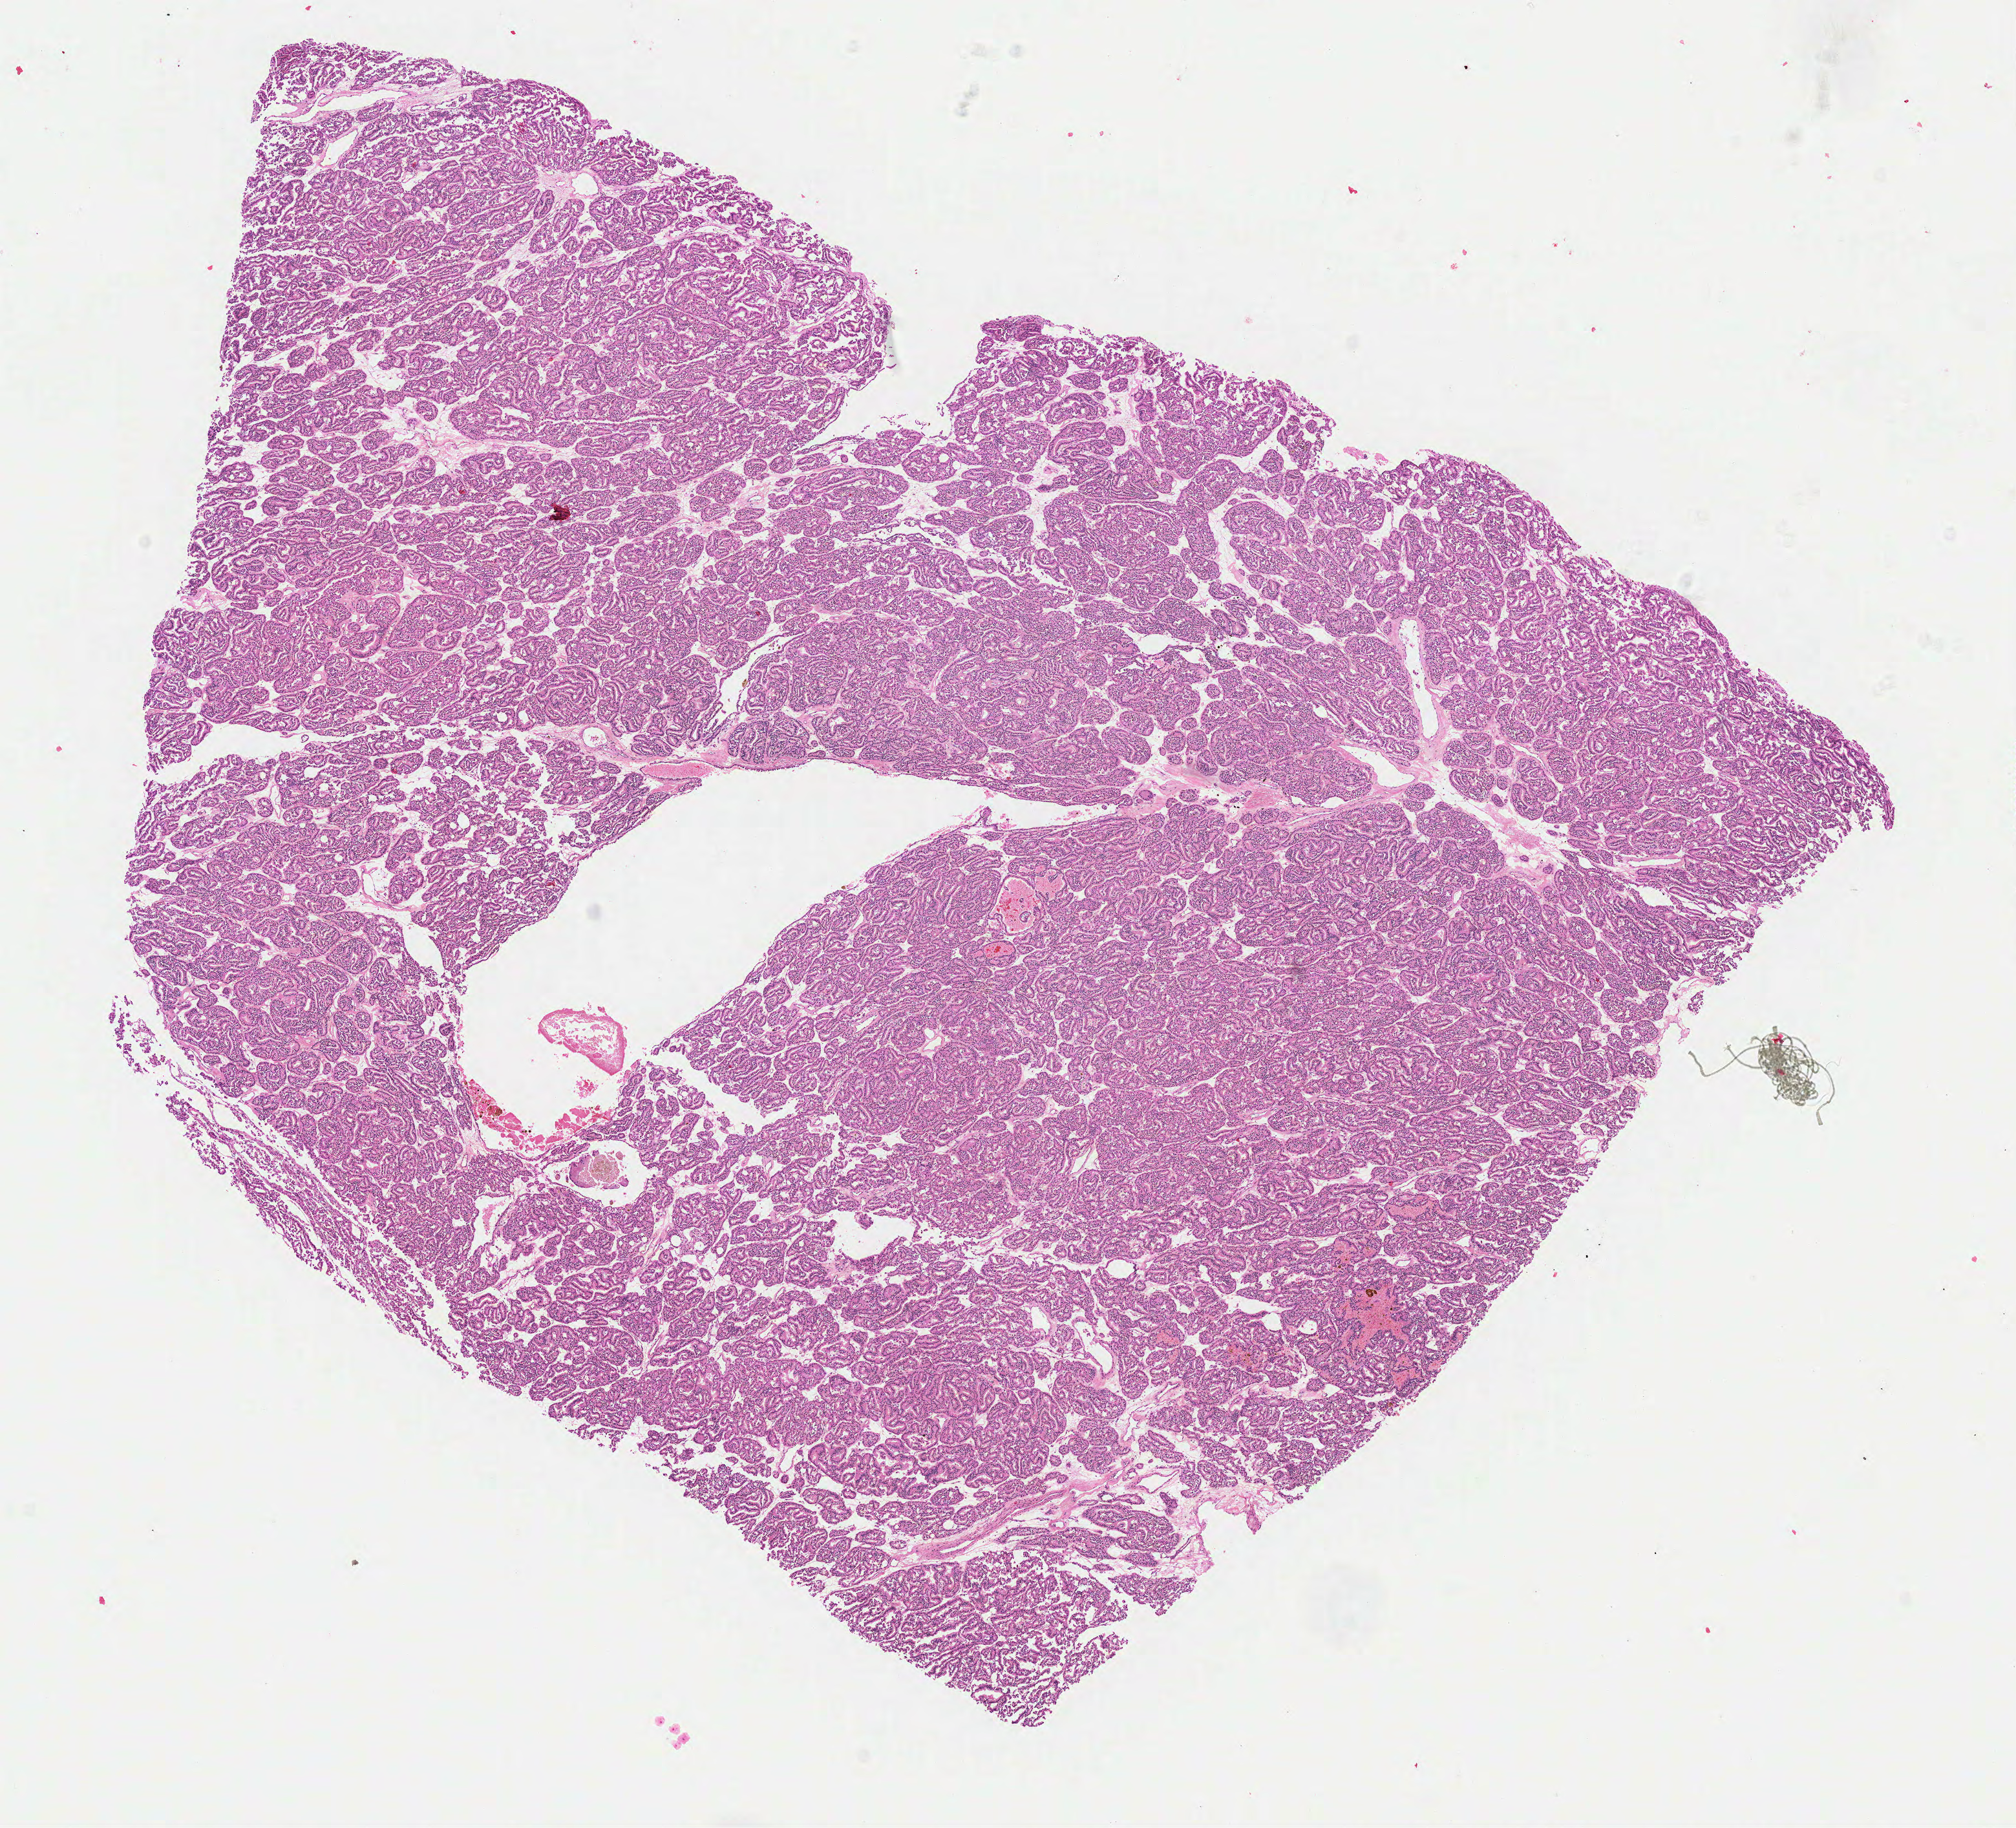
Whole-slide histology image, Hematoxylin and eosin (H&E) stained — a low-resolution overview of the entire scanned area, about 12.3 x 11.2 mm (from a 40x scan); formalin-fixed paraffin-embedded (FFPE) diagnostic section; primary tumour sample from the kidney. Male, age 45 years at initial diagnosis. Histologic grade: GX (grade cannot be assessed).
AJCC pathologic stage: II. Pathologic diagnosis: Clear cell adenocarcinoma, NOS.